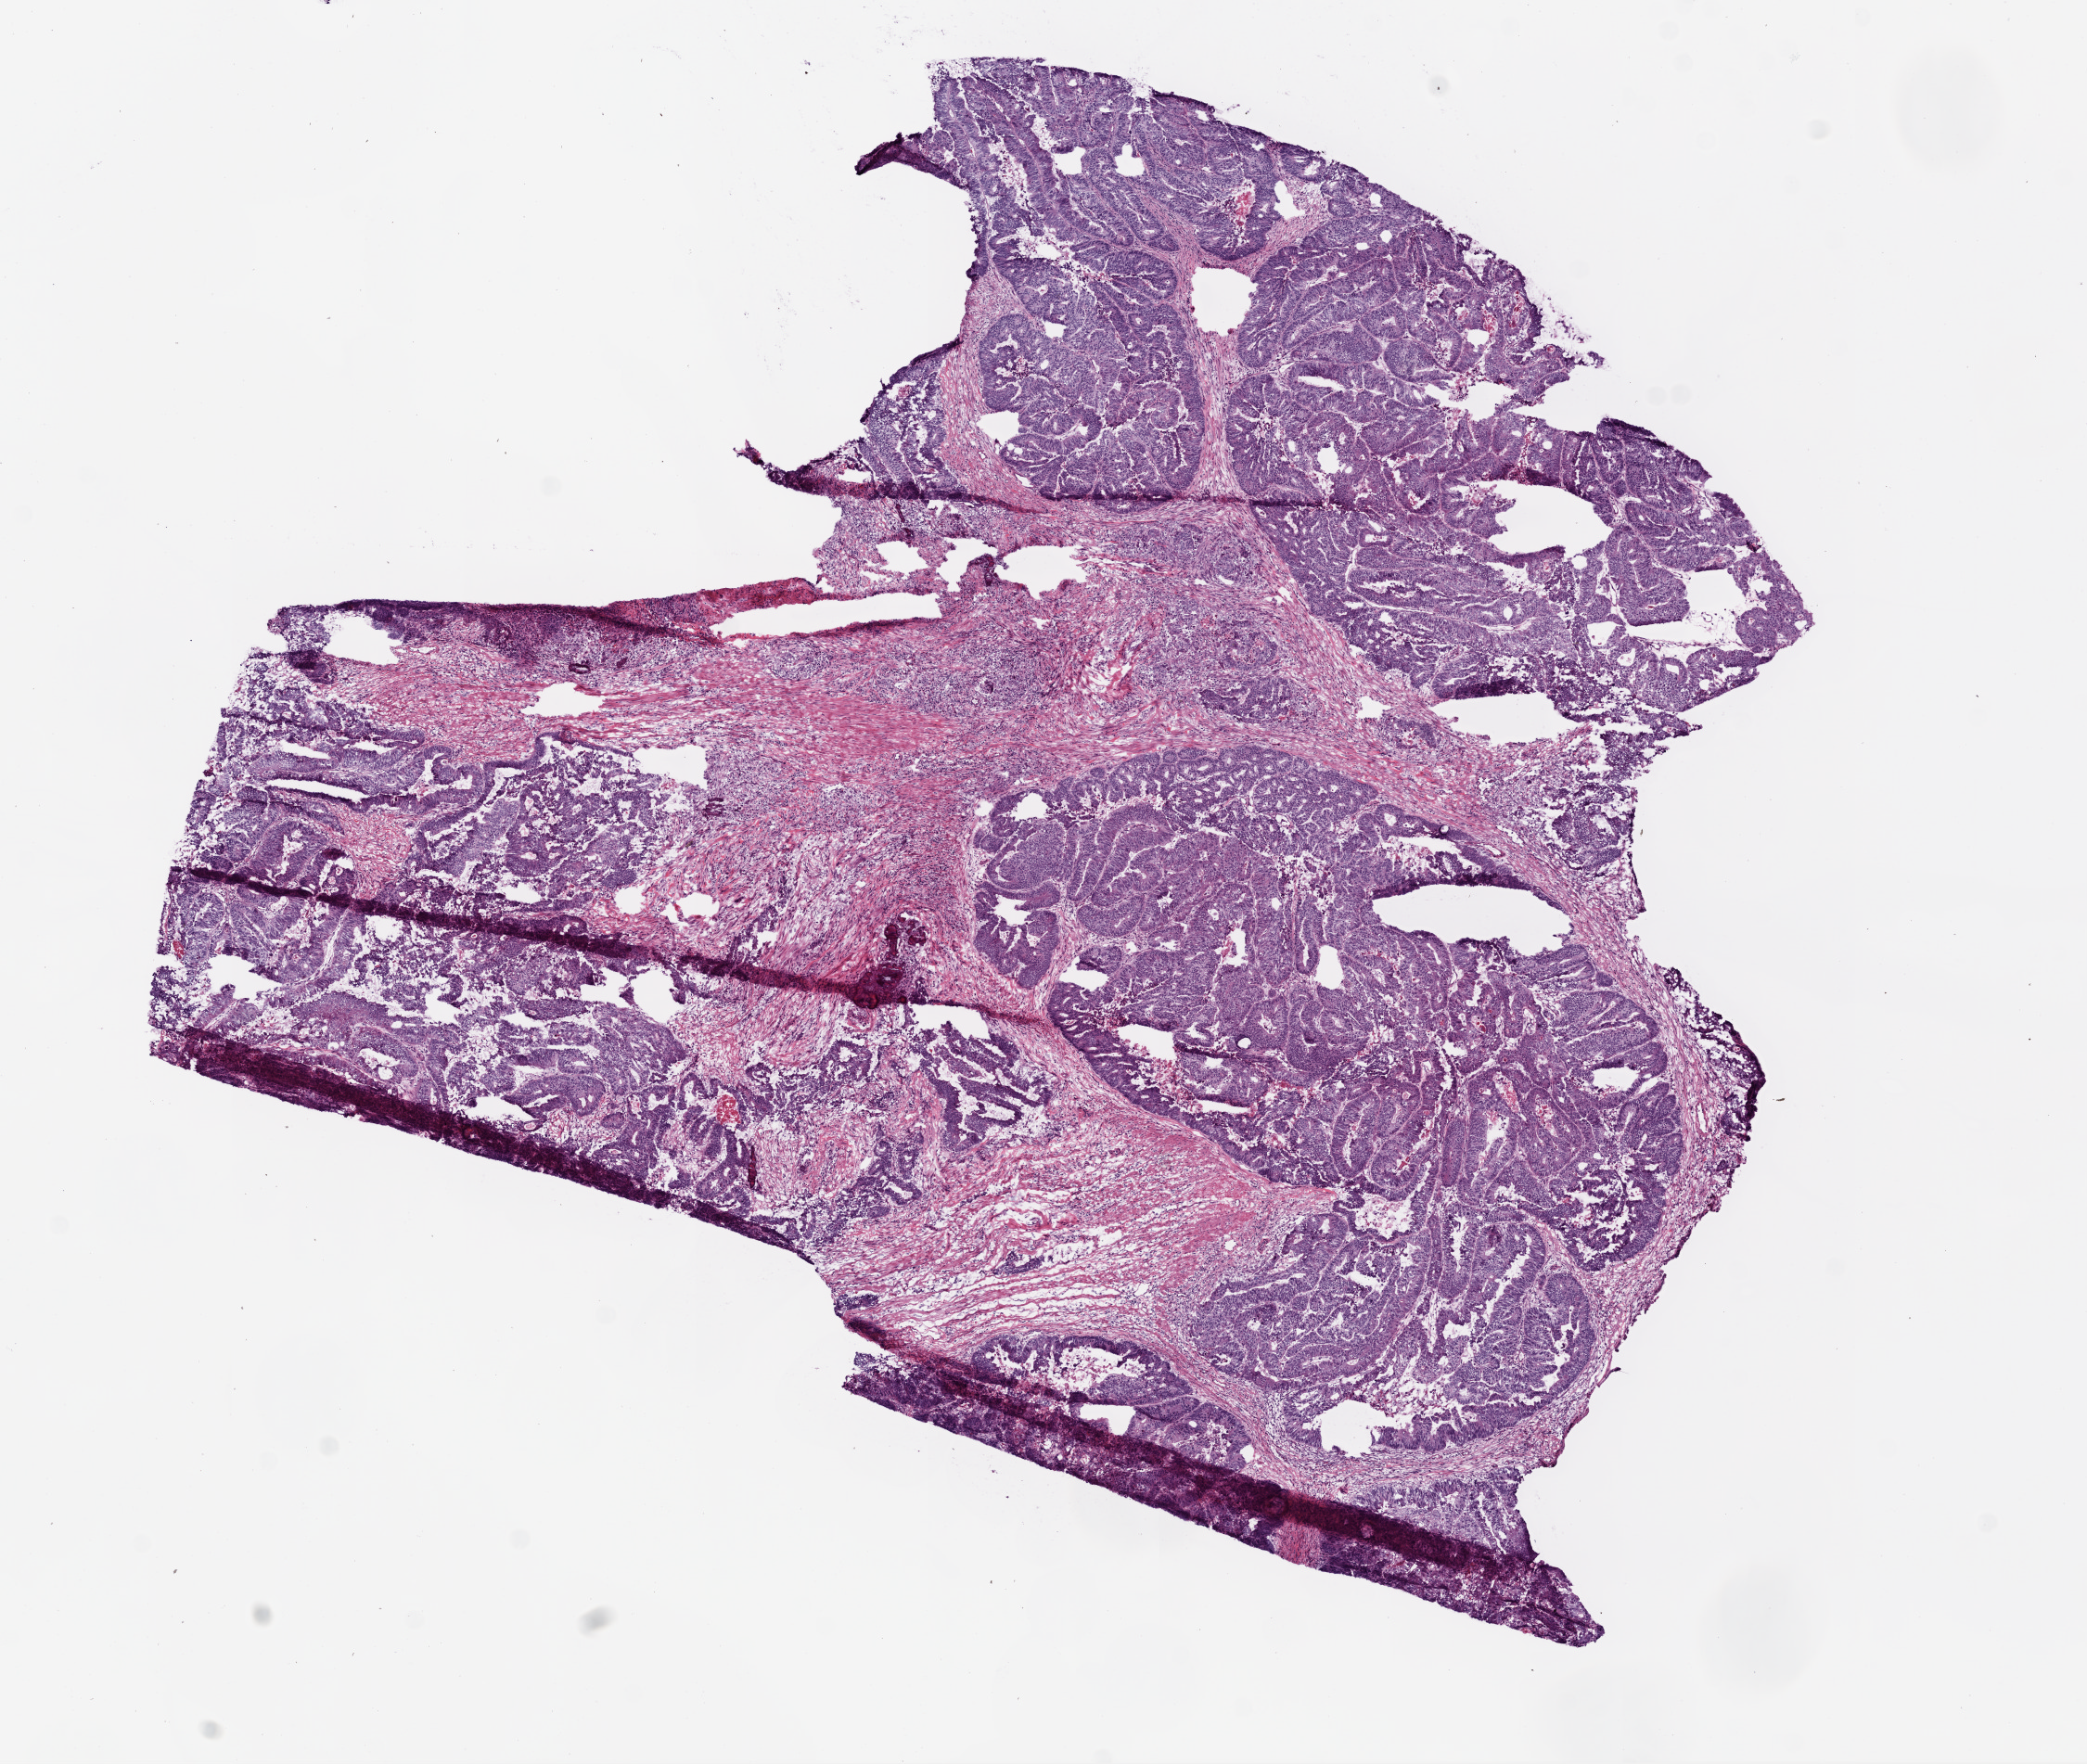
Digitized H&E-stained tissue section (whole slide), shown as a low-resolution overview of the whole scanned area (about 9.0 x 7.6 mm, from a 20x scan); frozen section; rectum, primary tumour sample. Female patient; age at initial diagnosis 85 years. Composition of this section per pathologist review: tumour cells 70%, tumour nuclei 65%, normal cells 0%, stromal cells 25%, necrosis 5%.
- histologic diagnosis: Adenocarcinoma, NOS (colon, NOS)
- AJCC pathologic stage: I
- lymph nodes positive (case pathology): 0 of 18 examined